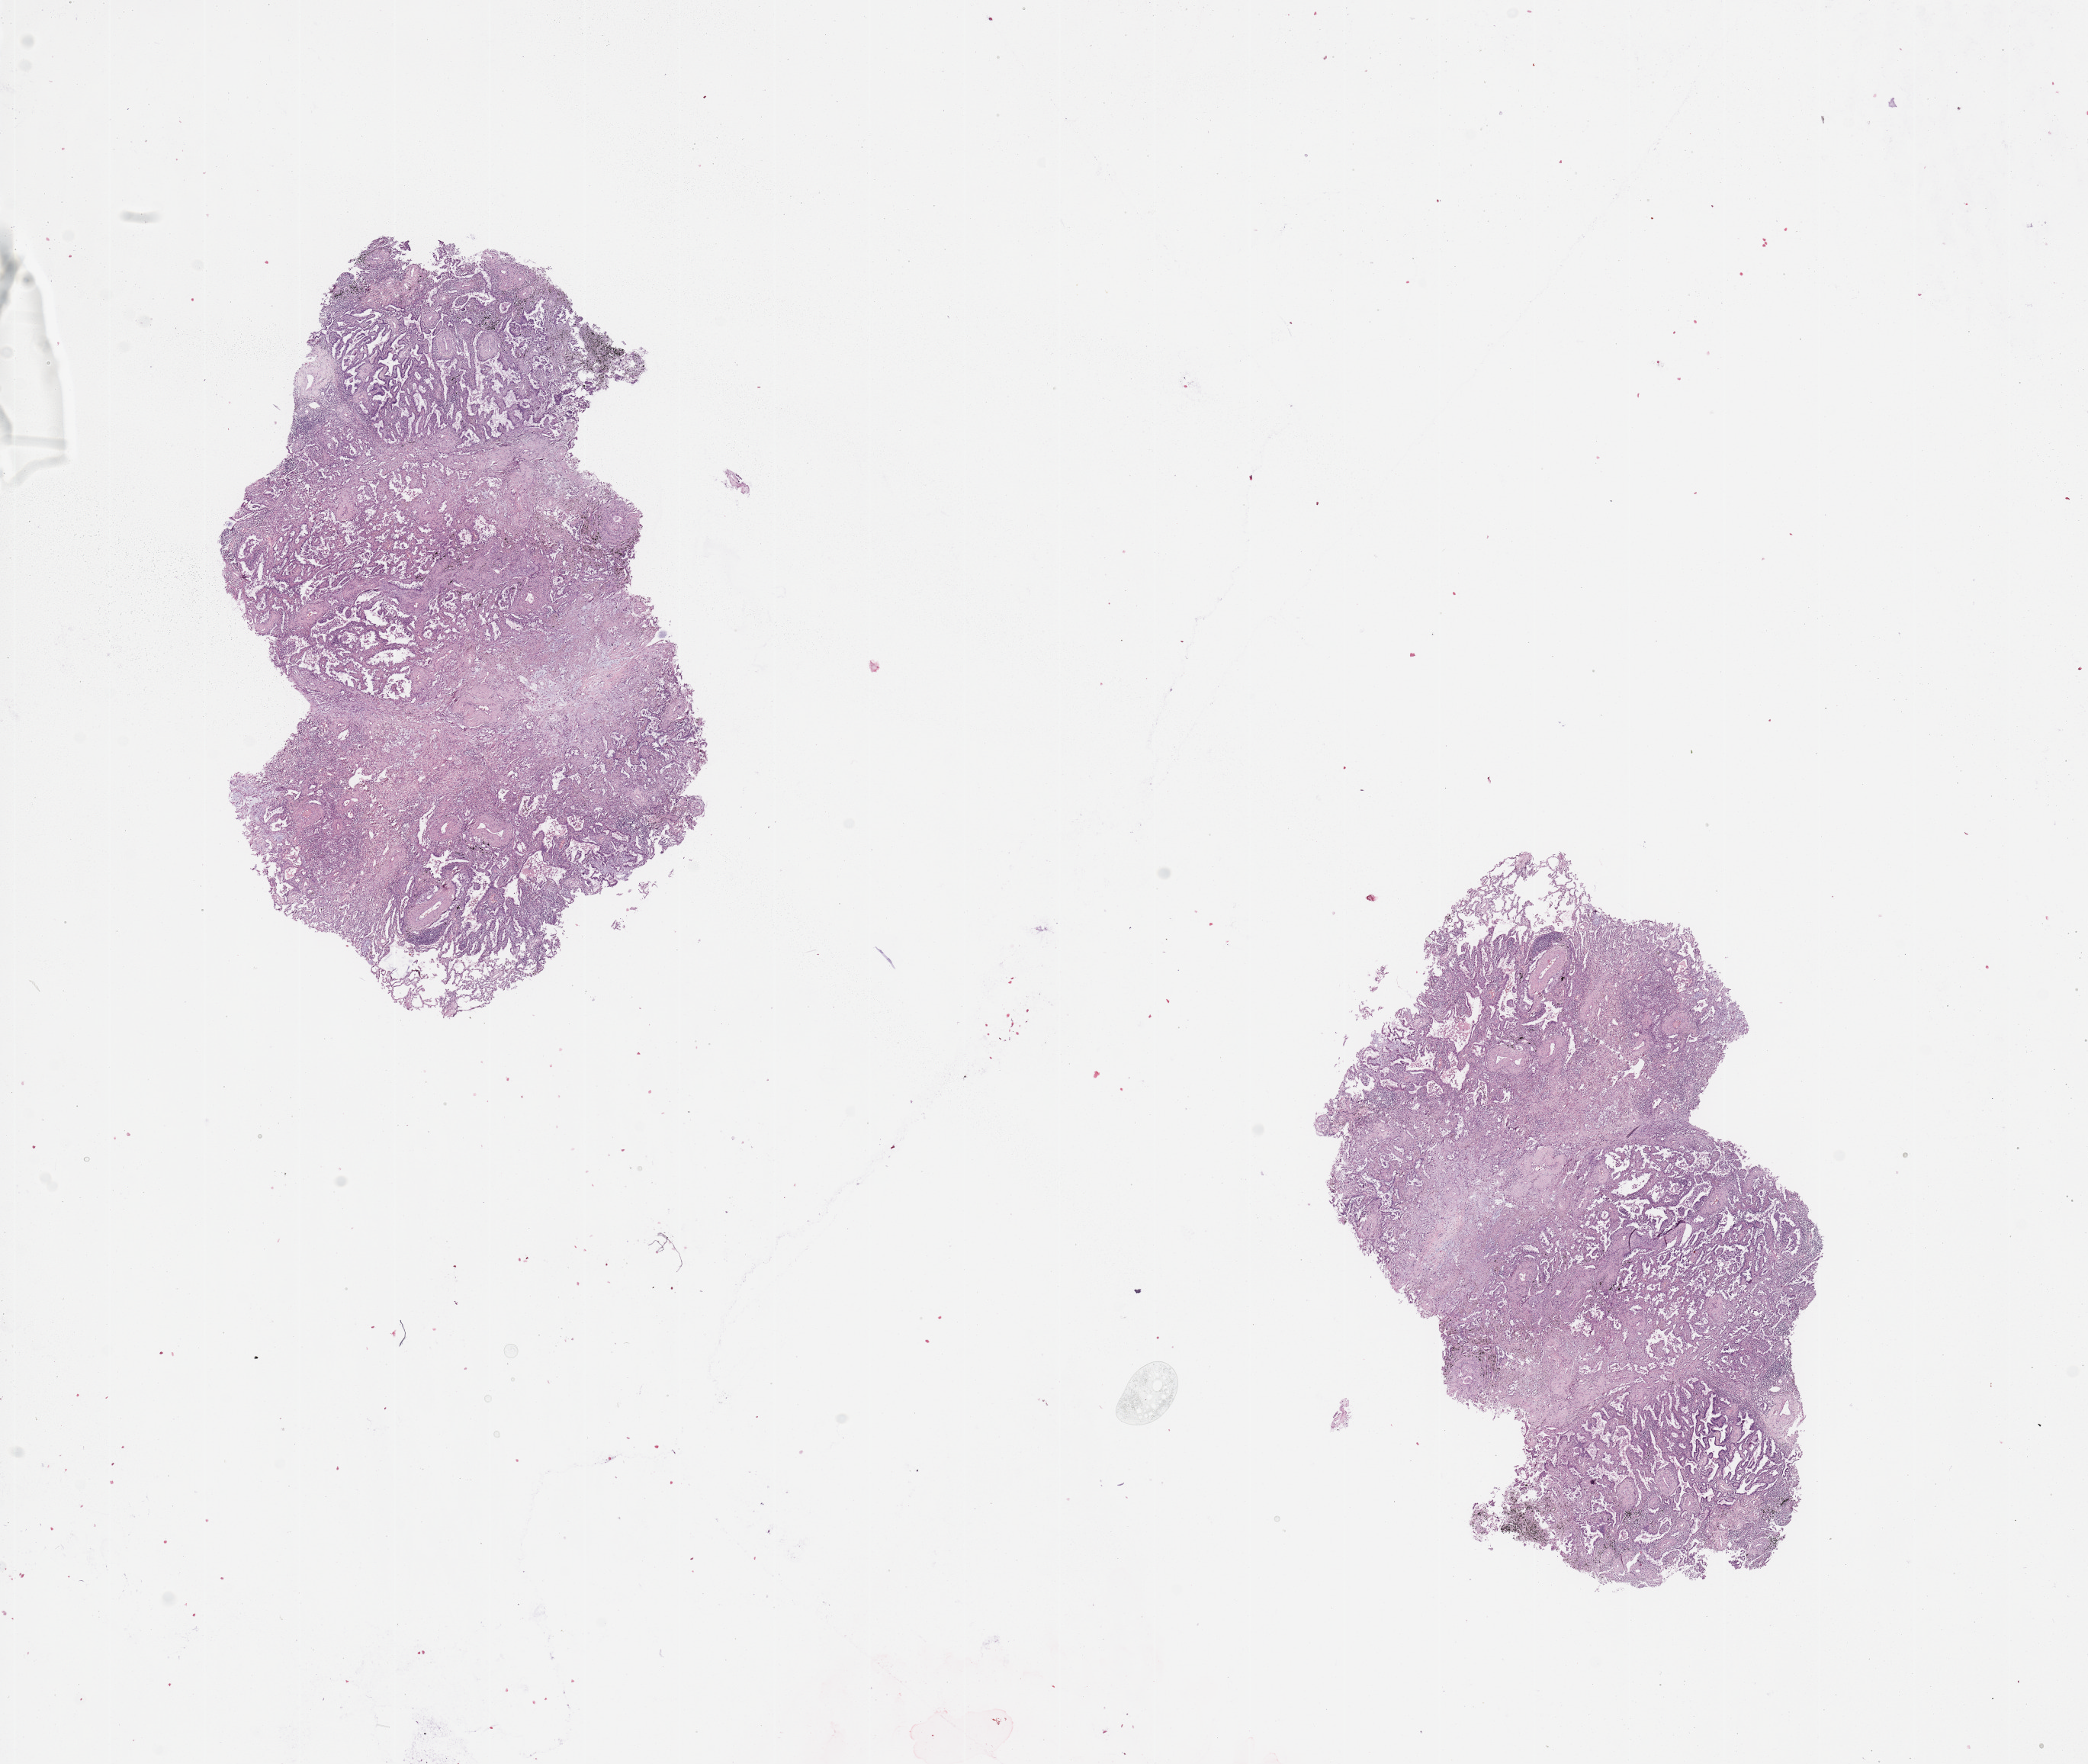
H&E-stained whole-slide image — low-resolution overview of the scanned area, about 21.7 x 18.3 mm (acquisition: 20x scan); lung, tumour tissue. 68-year-old male patient. Histologic grade: G2 (moderately differentiated).
• primary tumour site (as recorded): right middle lobe
• AJCC pathologic stage: IA
• histologic diagnosis: Adenocarcinoma, NOS